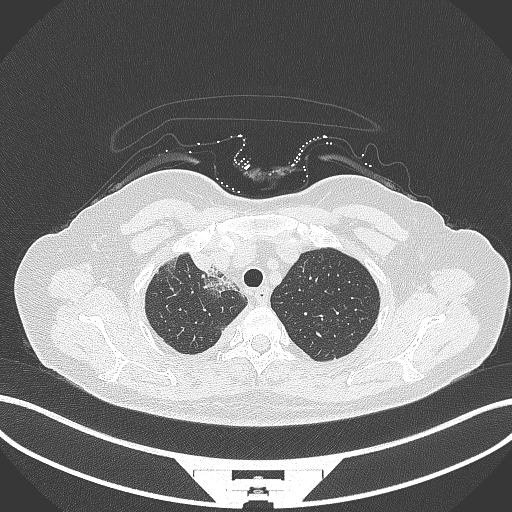
Chest CT, one axial slice; position 262 of 305 along the scan axis; reconstruction kernel B70f; 120 kVp; lung window (W 1500 / L -600 HU); 512 × 512 image matrix, field of view 400 × 400 mm. Female patient, age 52 years. Case-level facts recorded for this patient, not image findings: clinical TNM (as recorded): T3 N1 M1.
Annotated regions visible in this slice (rectangle marked by the reading radiologist):
- lung tumour (recorded histology: adenocarcinoma): bounding box <186,247,219,275> (left, top, right, bottom; pixels)